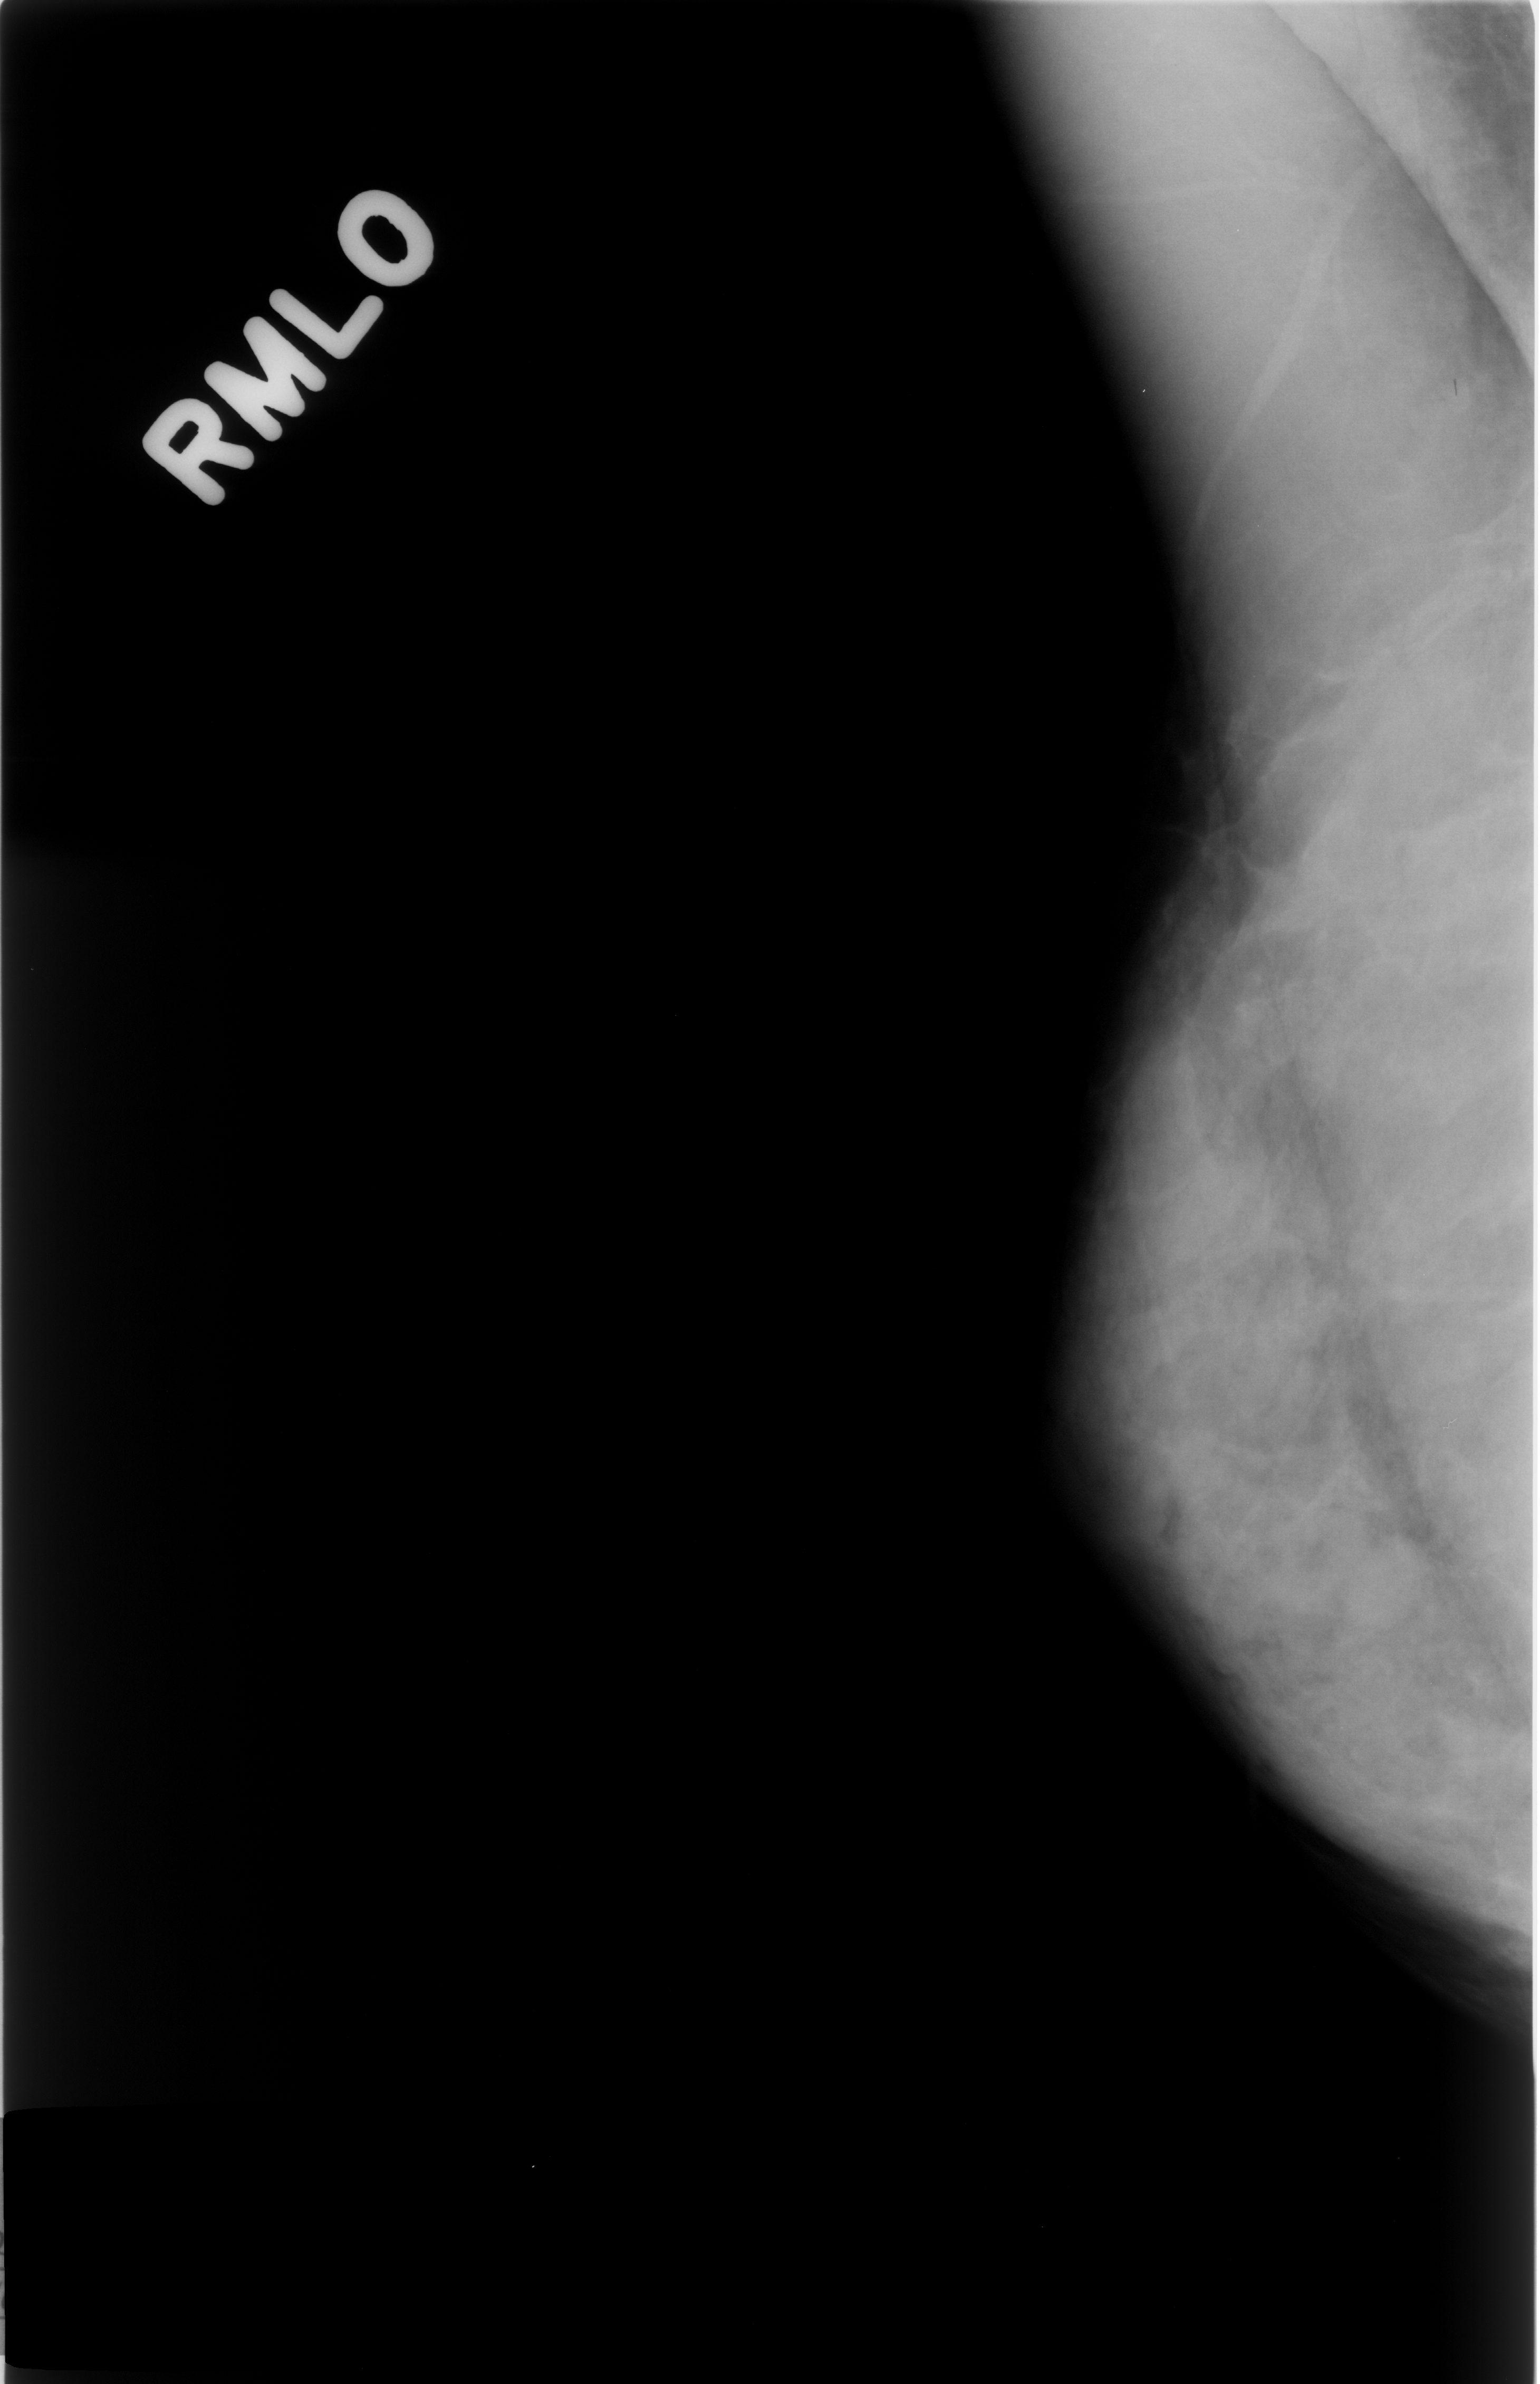
Scanned film-screen mammogram, right breast, mediolateral oblique (MLO) view, breast composition: extremely dense (BI-RADS density category 4 of 4).
Abnormality record for this image: mass, shape oval, margins circumscribed; BI-RADS assessment category 3; benign; no additional work-up was recommended (benign without callback).